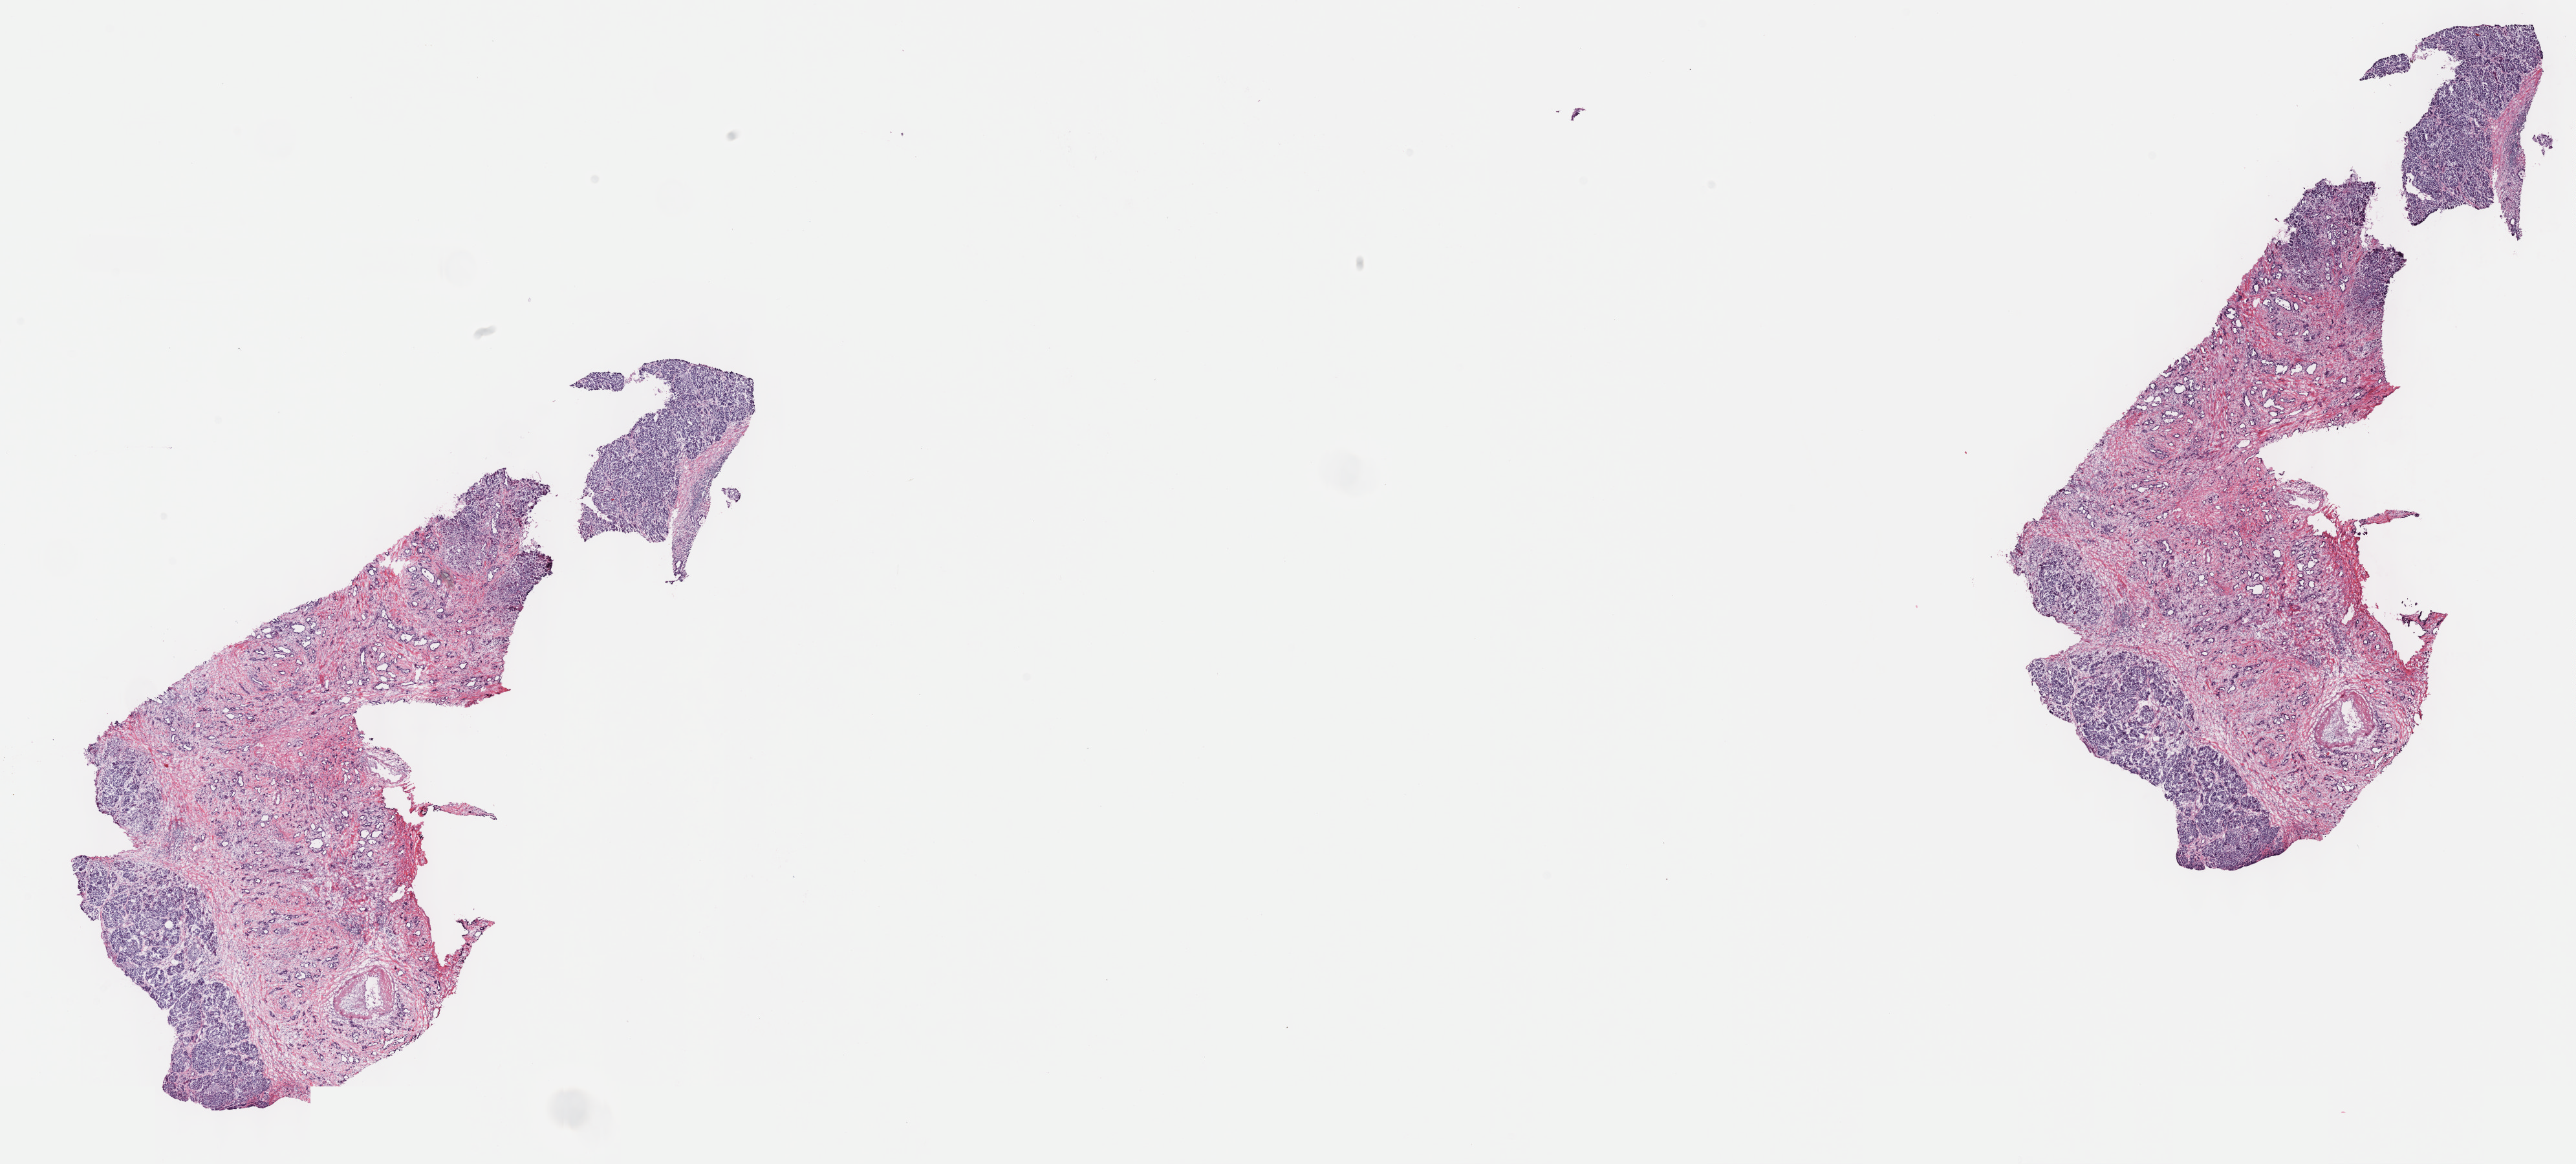
Whole-slide histology image, H&E — a low-resolution overview of the entire scanned area, about 32.2 x 14.6 mm (acquisition: 40x scan), frozen section from the top of the tissue portion, pancreas, primary tumour sample. Male patient; age at initial diagnosis 65 years. Histologic grade: G3 (poorly differentiated). Composition of this section per pathologist review: tumour cells 25%, tumour nuclei 35%, normal cells 40%, stromal cells 35%, necrosis 0%. Inflammatory infiltration, as recorded: lymphocyte infiltration 0%, monocyte infiltration 0%, neutrophil infiltration 0%.
Pathologic diagnosis: Infiltrating duct carcinoma, NOS (head of pancreas). AJCC pathologic stage: IIB (7th edition). TNM: T3 N1 M0. Lymph nodes positive (case pathology): 16 of 19 examined.